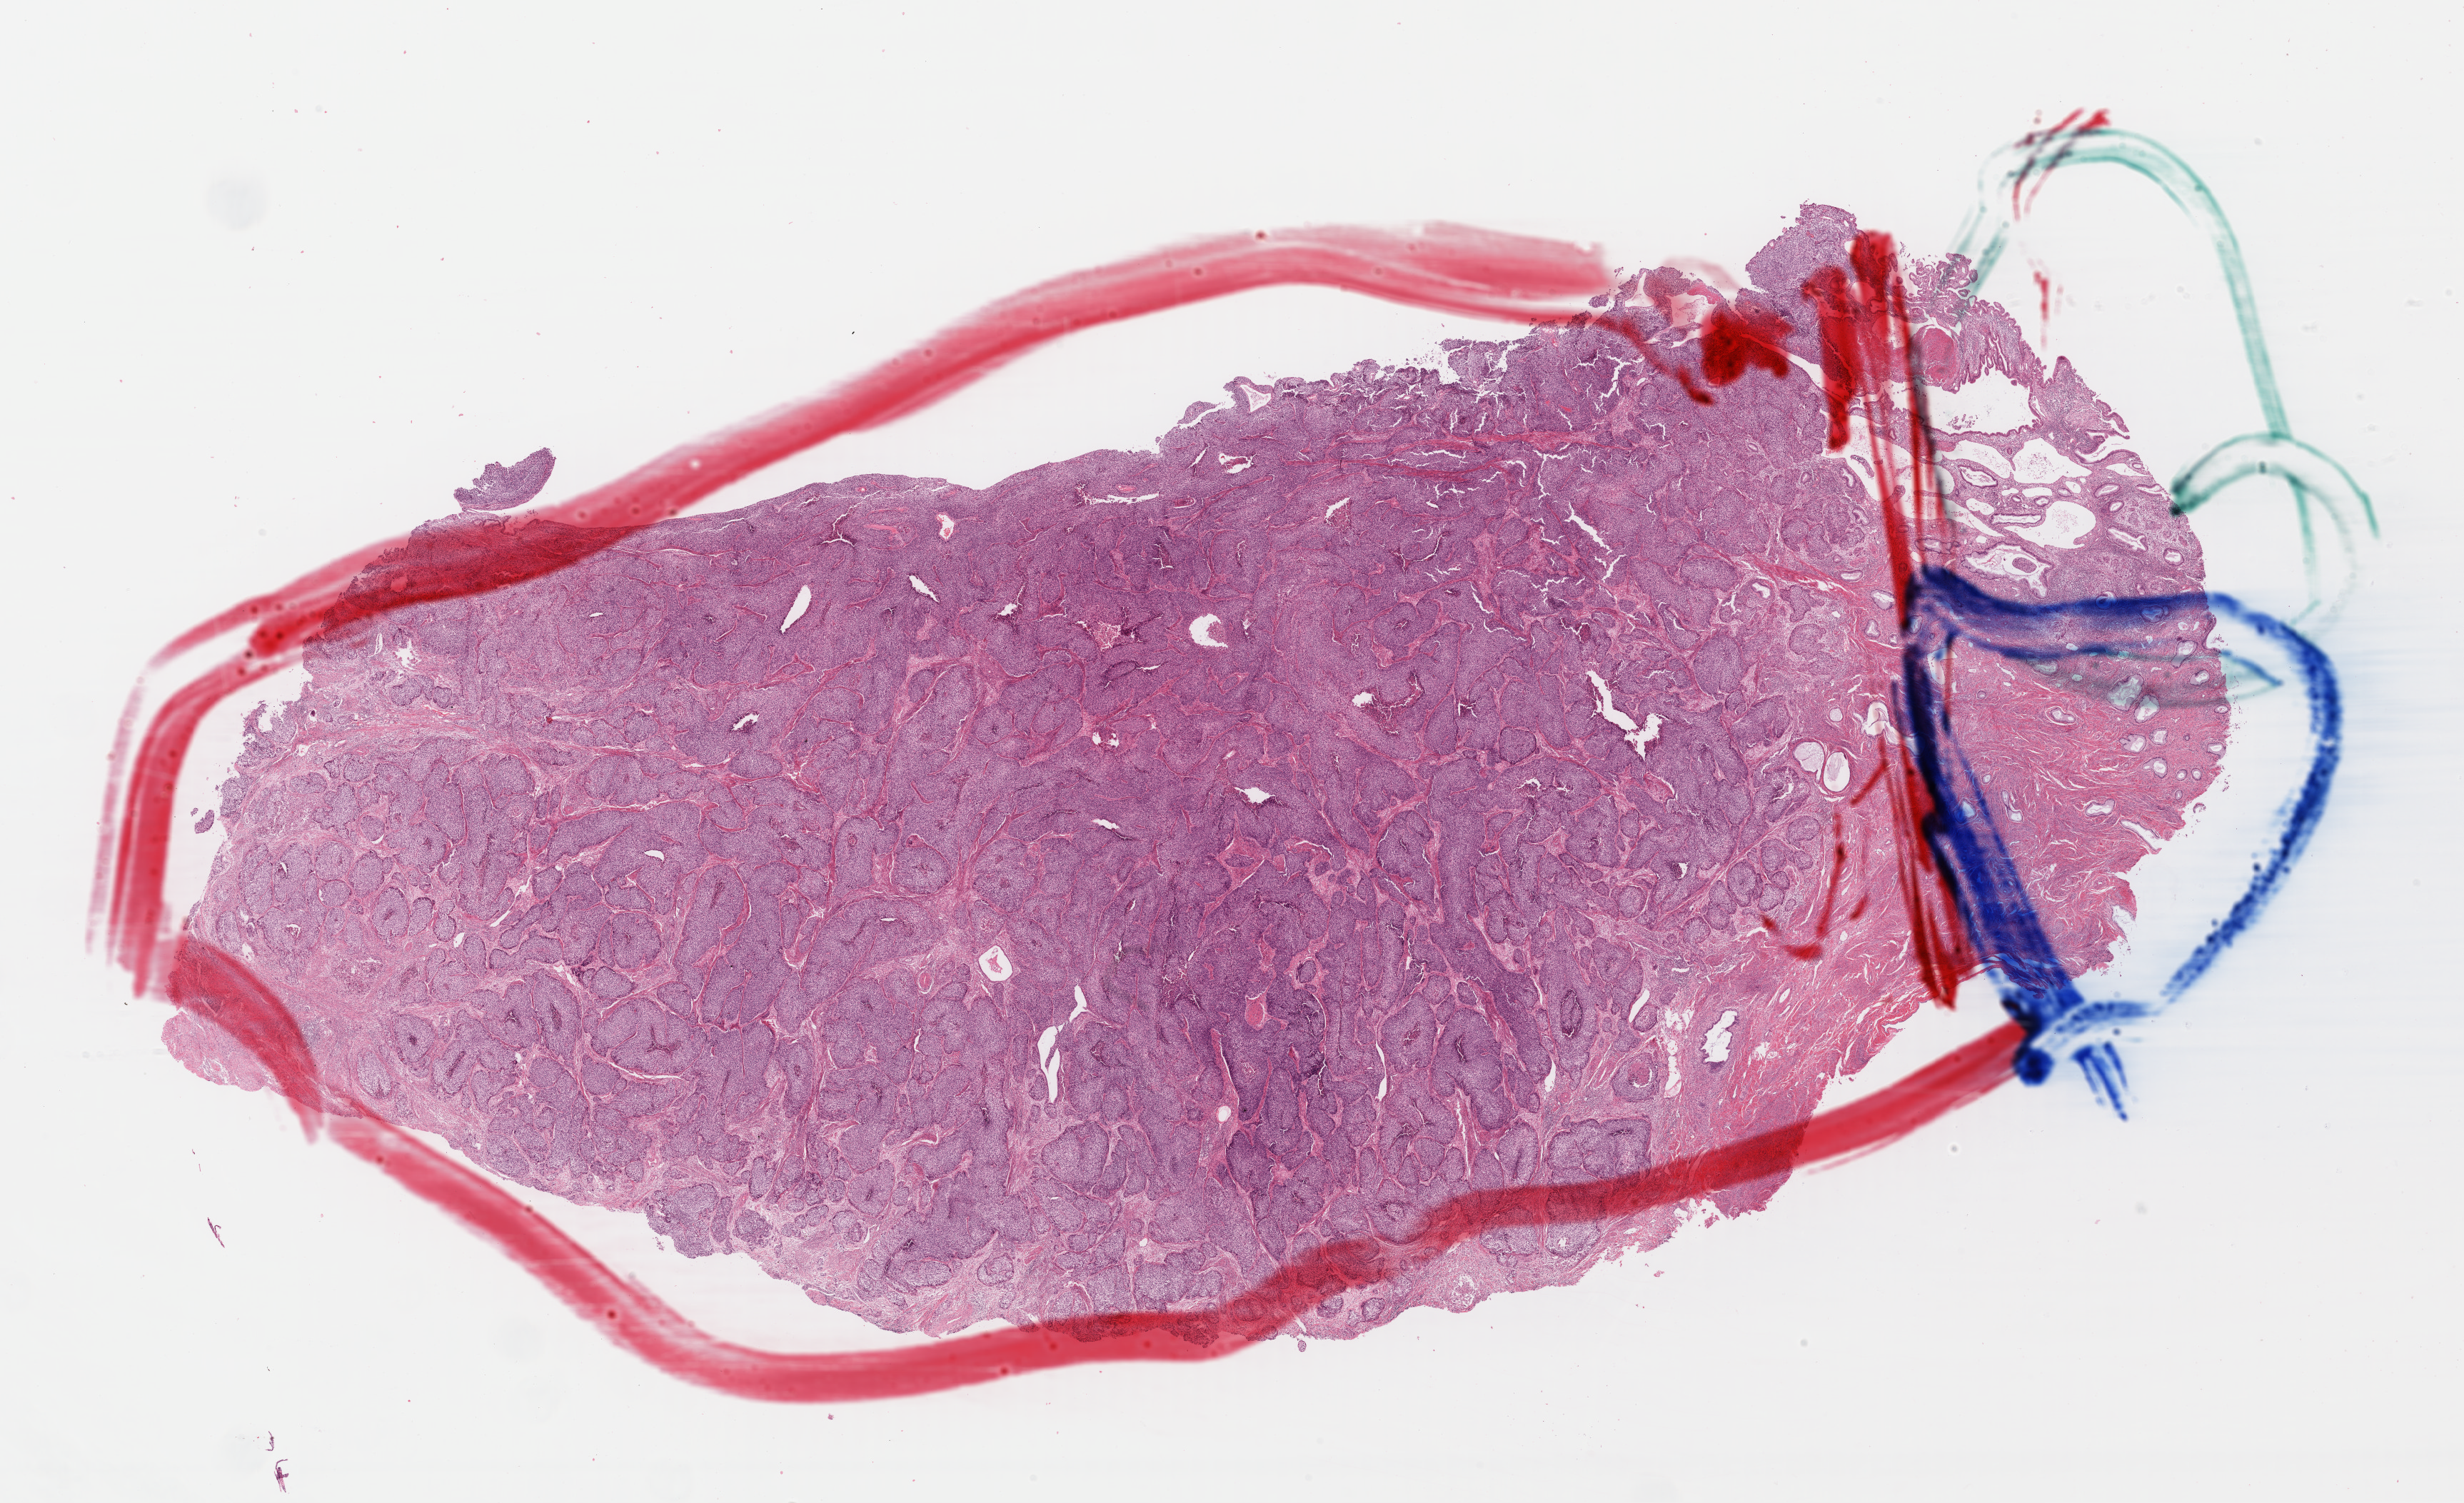
Digitized Hematoxylin and eosin (H&E) stained tissue section (whole slide), low-resolution overview of the scanned area, about 27.1 x 16.5 mm (slide scanned at 40x); formalin-fixed paraffin-embedded (FFPE) diagnostic section; primary tumour sample from the cervix. Female patient; age at initial diagnosis 47 years. Histologic grade: G2 (moderately differentiated).
- FIGO stage: IB
- diagnosis: Squamous cell carcinoma, large cell, nonkeratinizing, NOS (cervix uteri)
- lymph nodes positive (case pathology): 0 of 18 examined